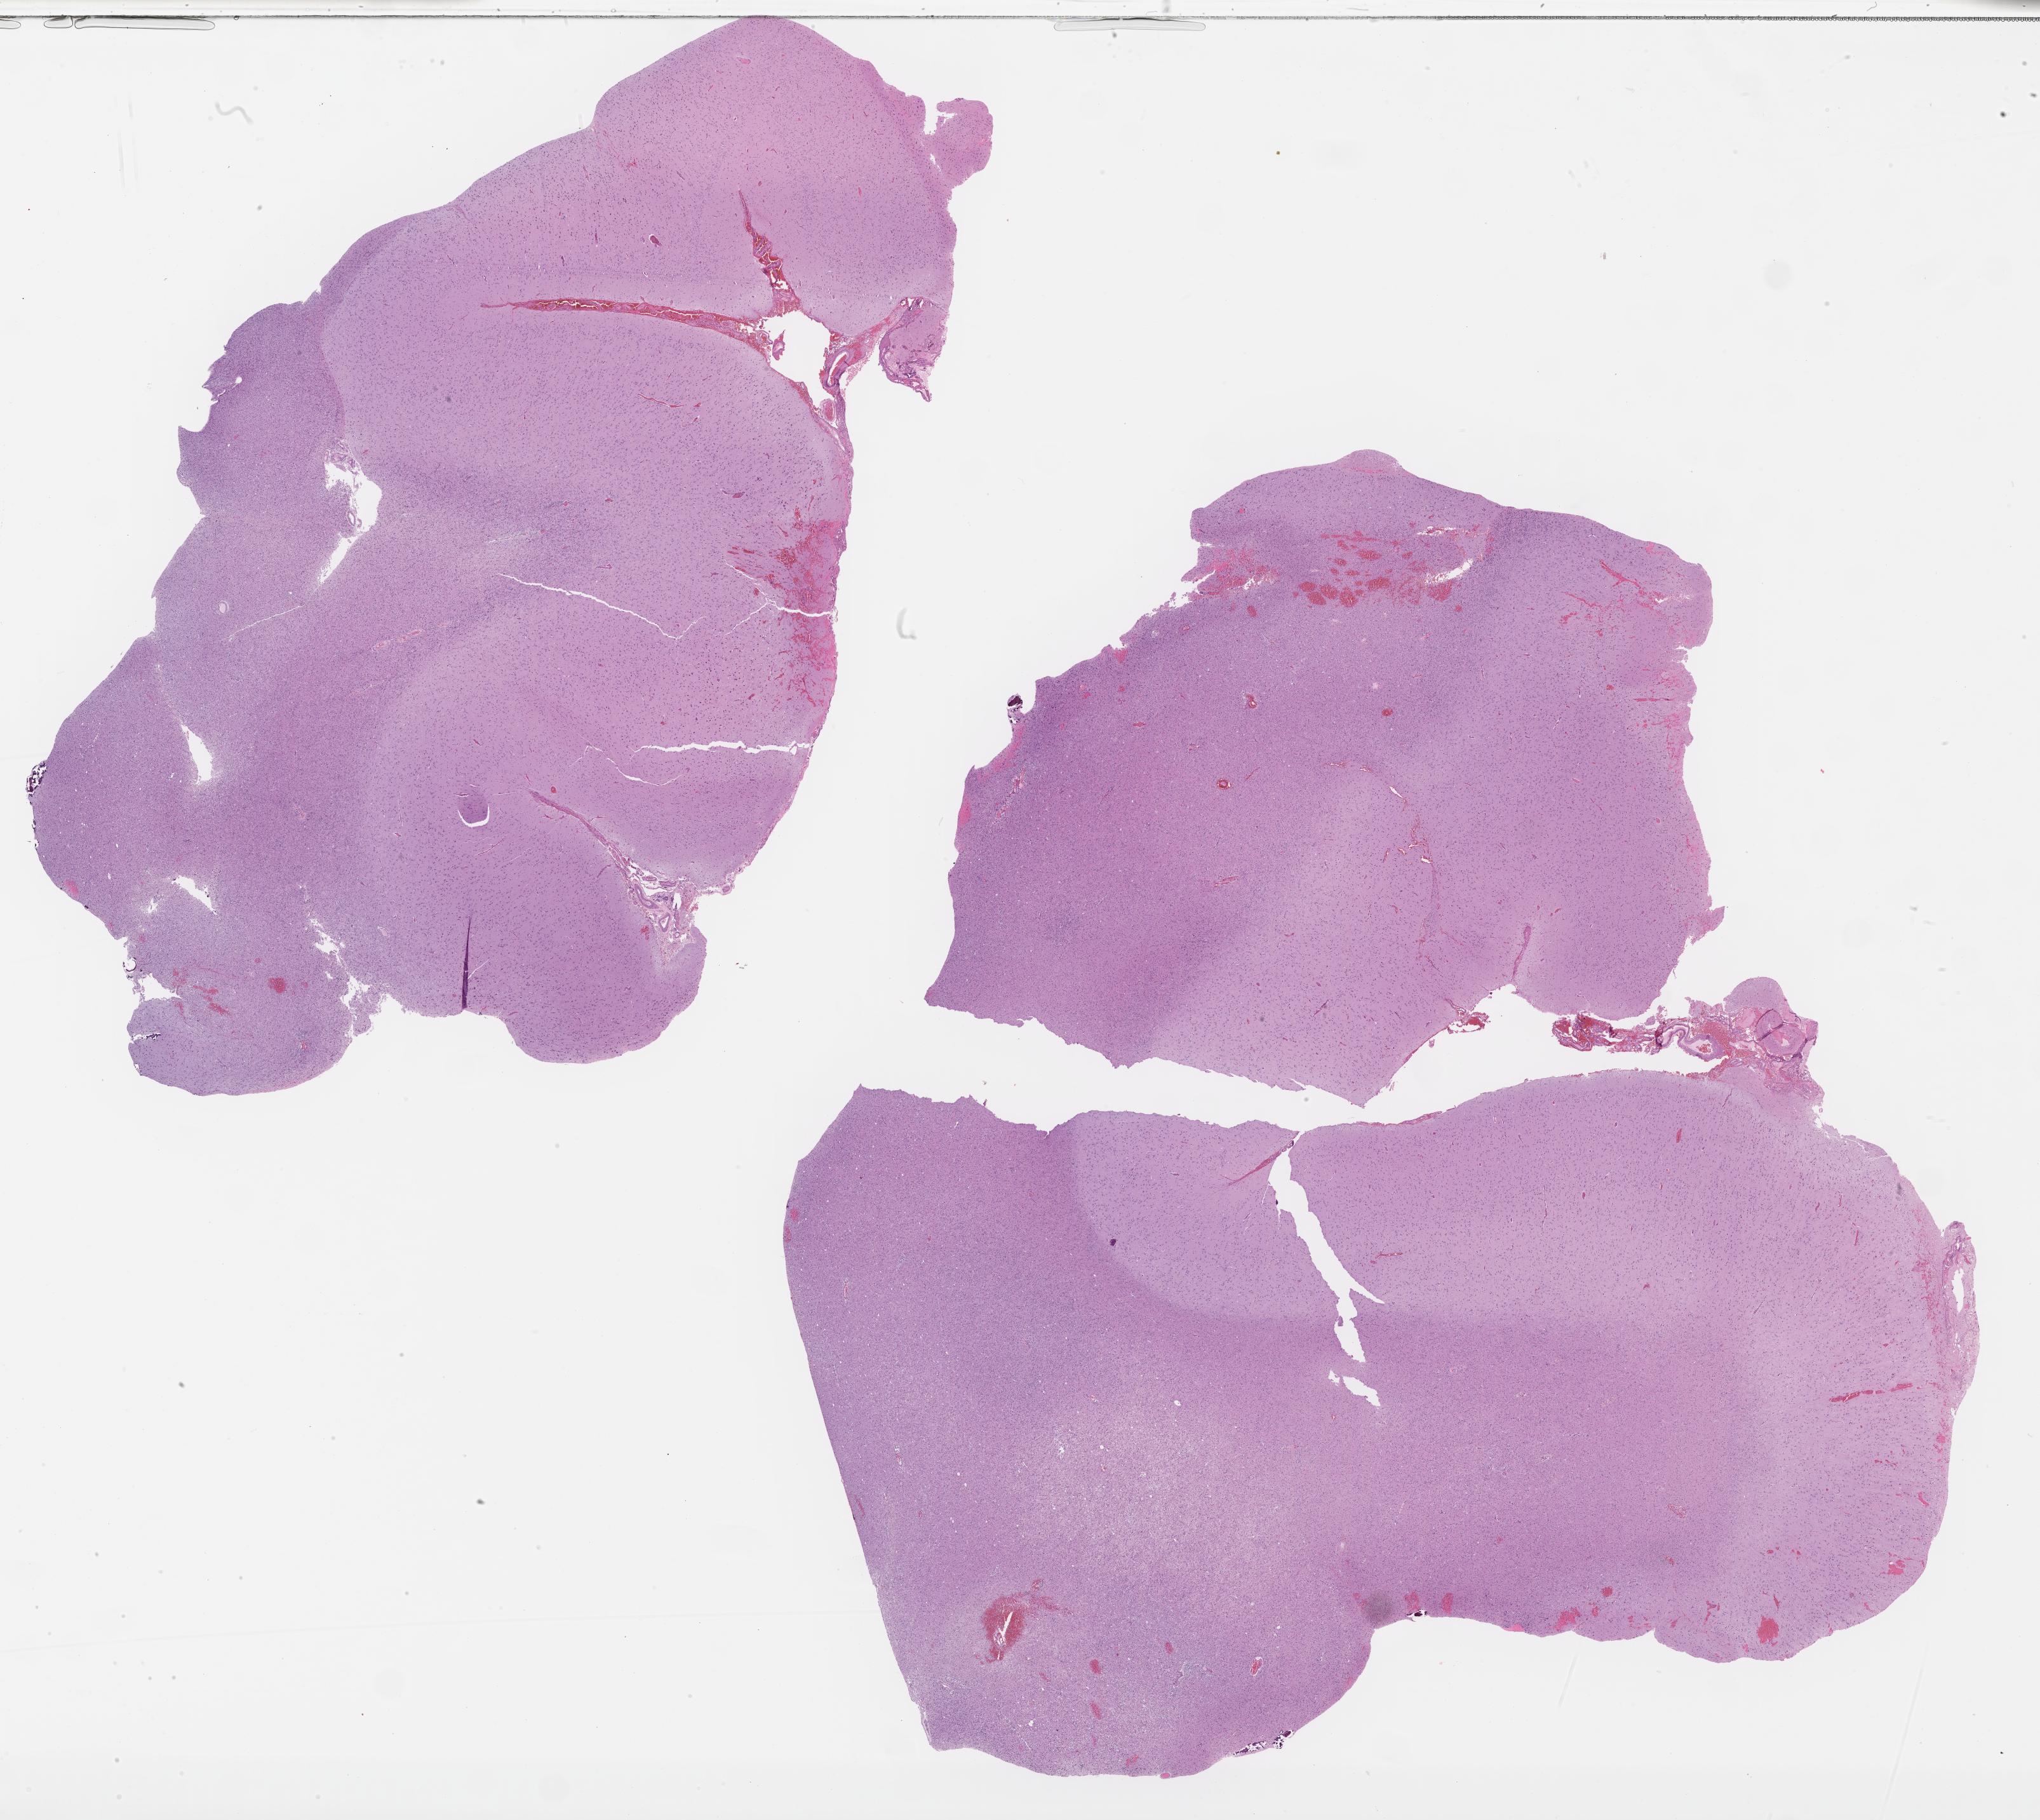
Digitized Hematoxylin and eosin (H&E) stained tissue section (whole slide) — whole scanned area (about 25.9 x 23.1 mm, acquisition: 40x scan) shown as a low-resolution overview; formalin-fixed paraffin-embedded (FFPE) diagnostic section; brain, primary tumour sample. Patient: female, age at initial diagnosis 53 years. Histologic grade: G2 (moderately differentiated).
* histologic diagnosis: Oligodendroglioma, NOS (cerebrum)